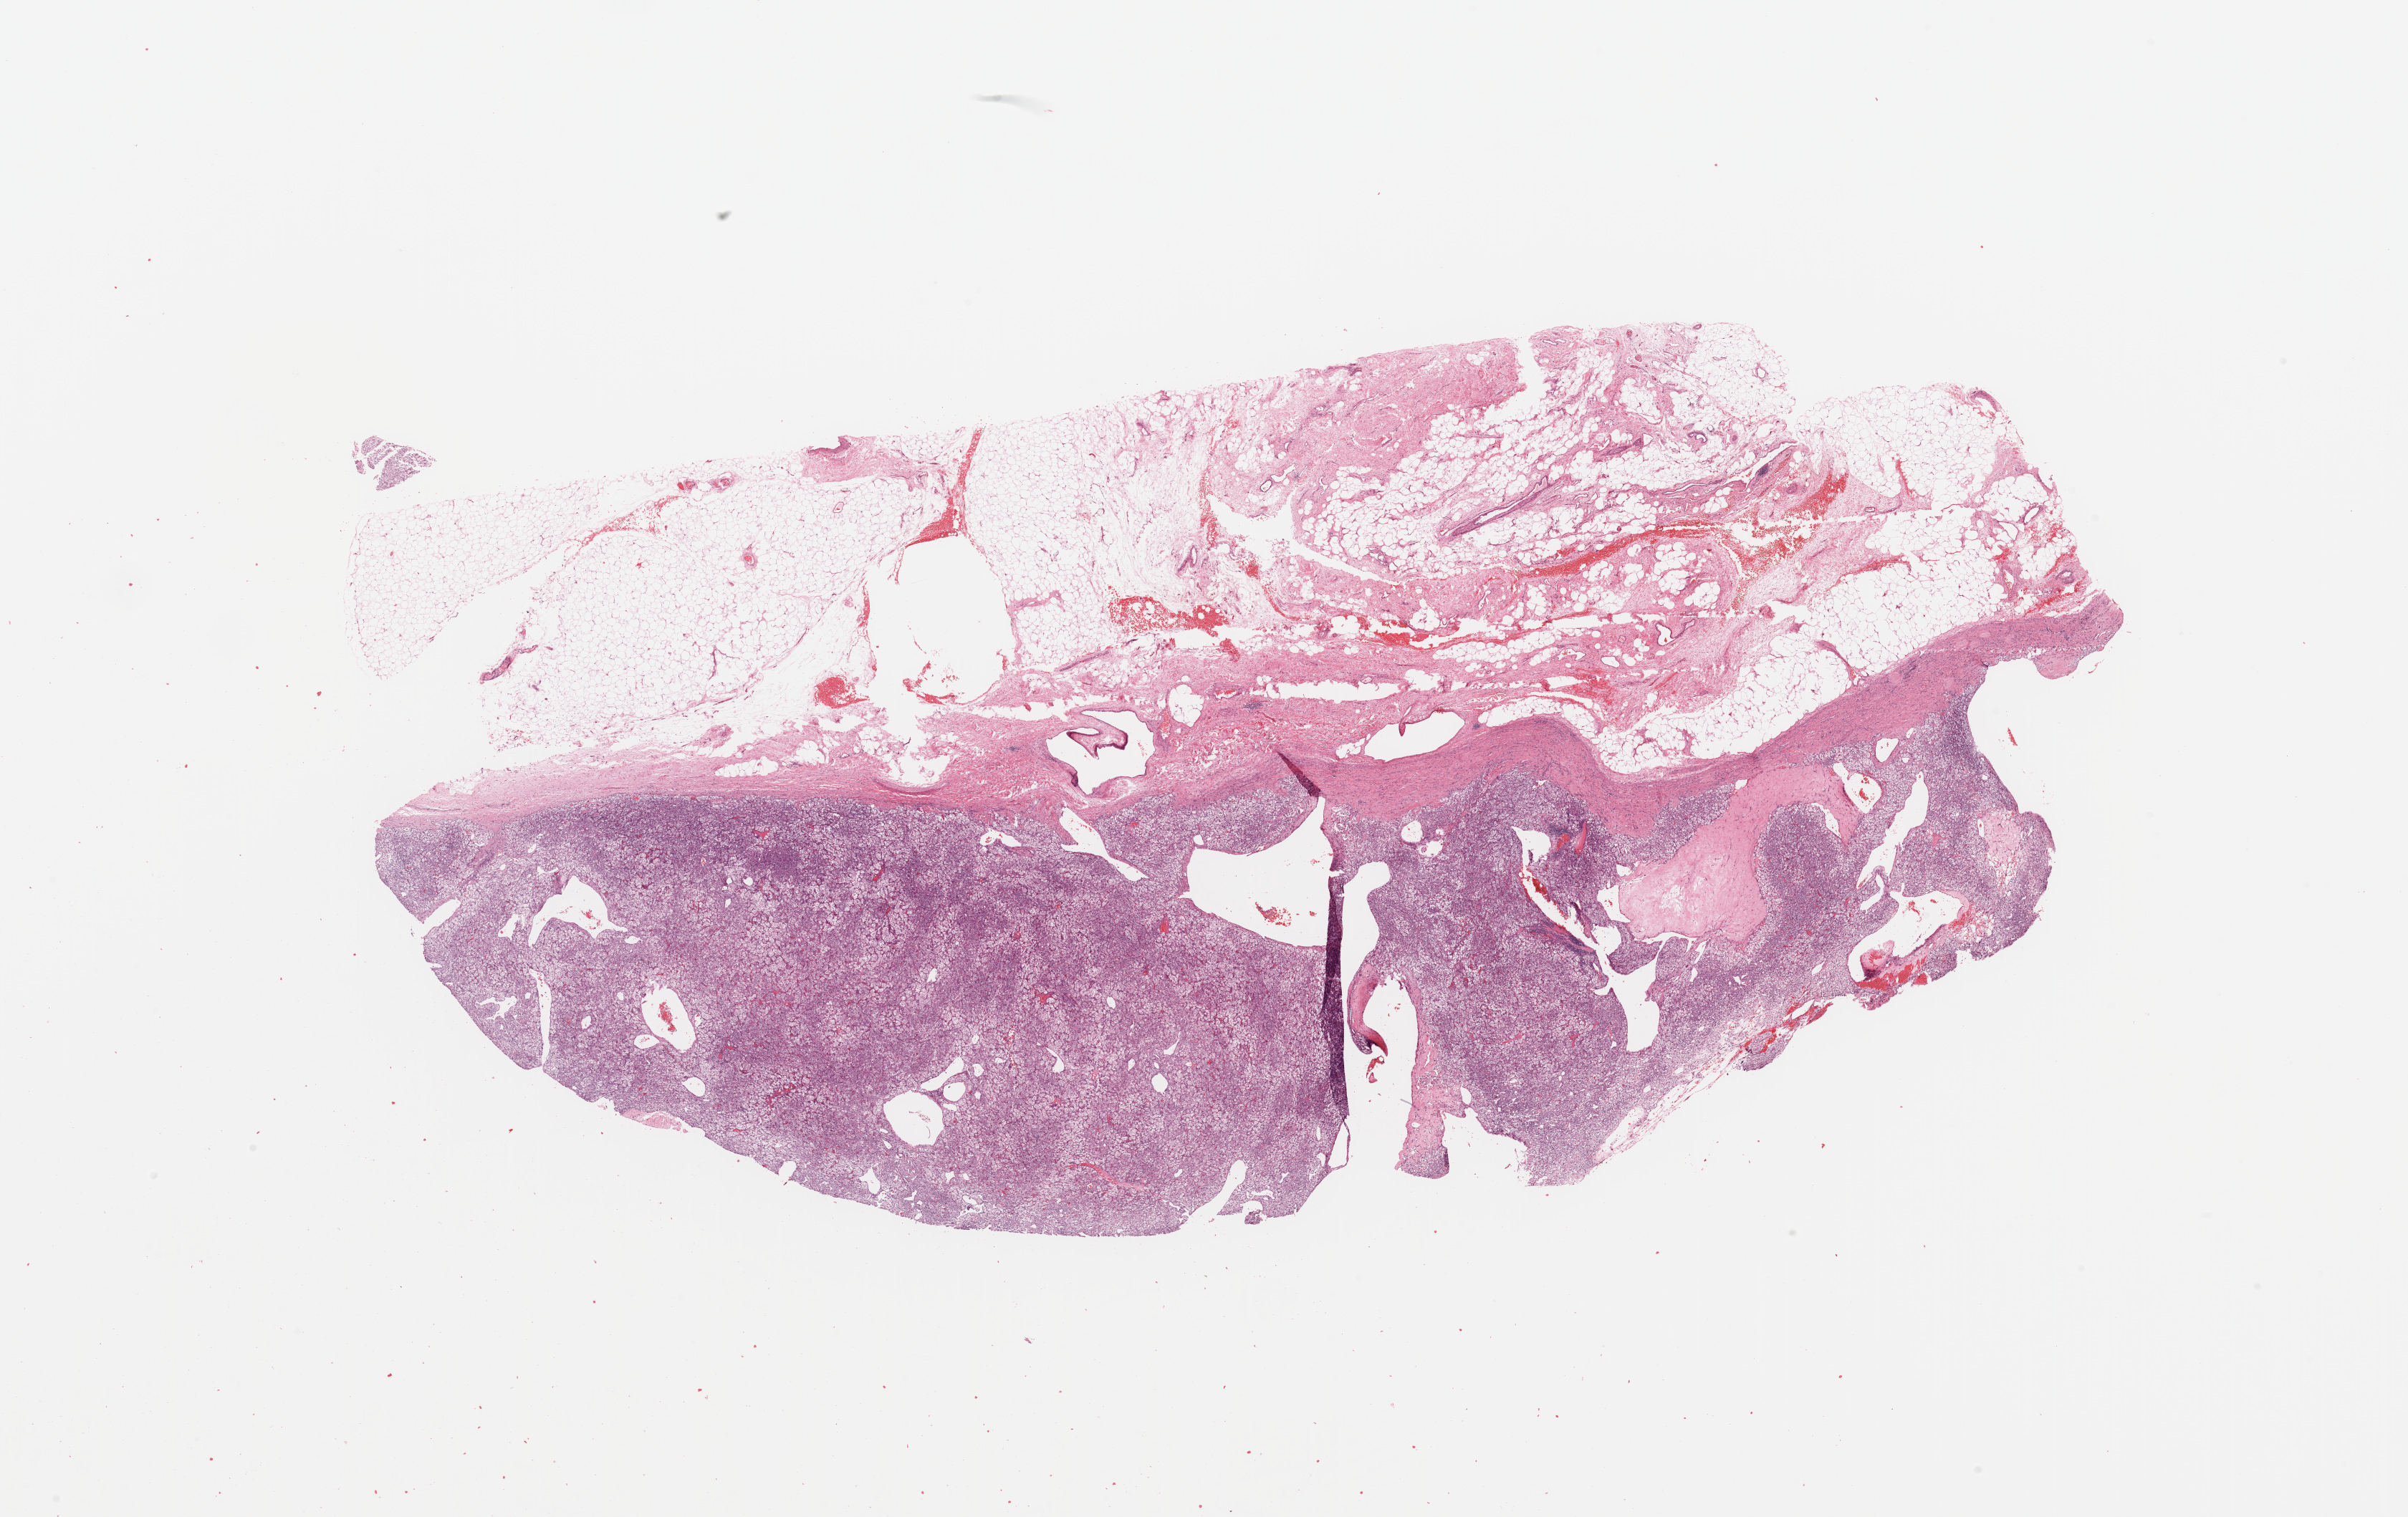
Digitized H&E tissue section (whole slide), low-resolution overview of the scanned area, about 26.6 x 16.7 mm (acquisition: 20x scan). Kidney, tumour tissue. Patient: female, age 76 years. Histologic grade: G2 (moderately differentiated).
Diagnosis: Renal cell carcinoma, NOS.